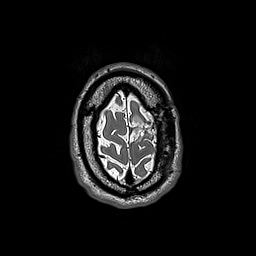
Brain MRI from a brain-tumour surgery series, one axial slice. Slice 36 of 192 in the series (ordered by position). 1 mm slice thickness. 256 × 256 image matrix. From the clinical record (not read from this slice): histopathology: Oligodendroglioma; WHO grade: 3; IDH mutation: yes.
Outlined on this slice (expert manual segmentation):
- tumour: bounding box [x1, y1, x2, y2] px = [133, 116, 146, 132]